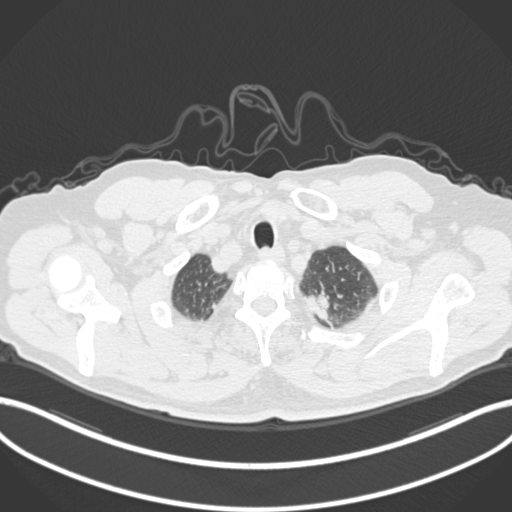
Chest CT, one axial slice; position 292 of 306 along the scan axis; 120 kVp; lung window (W 1500 / L -600 HU); 512 × 512 image matrix, field of view 400 × 400 mm. Patient: male, 64 years. From the clinical record (not read from this slice): clinical TNM (as recorded): T1c N0 M0.
Structures marked on this image (bounding box drawn by a radiologist):
- lung tumour (recorded histology: adenocarcinoma): bounding box [x1, y1, x2, y2] px = [303, 288, 333, 322]